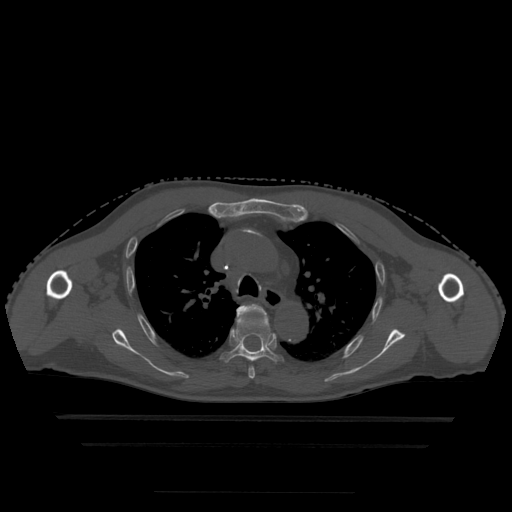
CT including the spine, one axial slice. Position 341 of 522 along the scan axis. Bone window (W 1800 / L 400 HU). 1.25 mm slice thickness. 512 × 512 image matrix, field of view 436 × 436 mm. Patient age 68 years. Case-level facts recorded for this patient, not image findings: primary cancer: urothelial.
Annotated regions visible in this slice (semi-automatically segmented with operator editing):
- T4 vertebra: bounding box [x1, y1, x2, y2] px = [237, 304, 265, 379]
- T5 vertebra: [221, 310, 283, 362]